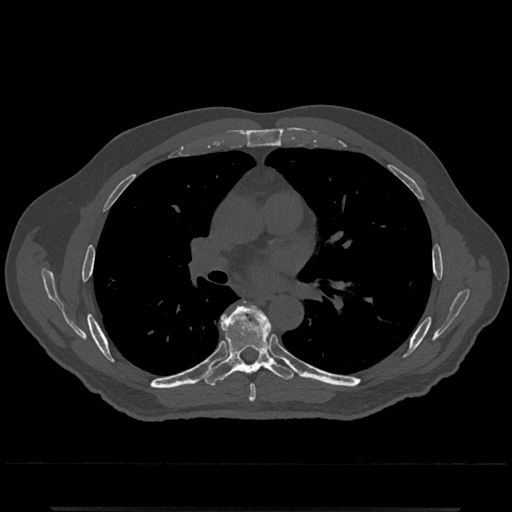
CT including the spine, one axial slice. Position 738 of 797 along the scan axis. Reconstruction kernel Br40s/3. Bone window (W 1800 / L 400 HU). 0.5 mm slice thickness. 512 × 512 image matrix, field of view 393 × 393 mm. Male patient, age 67 years. Case-level facts recorded for this patient, not image findings: primary cancer: prostate.
Outlined on this slice (semi-automatic segmentation, software-assisted and operator-edited):
- T6 vertebra: bounding box (x1, y1, x2, y2) in pixels: (249, 385, 256, 402)
- T7 vertebra: (201, 304, 295, 386)